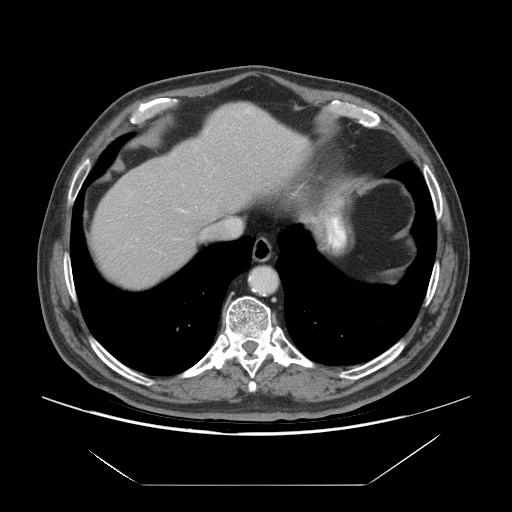
Contrast-enhanced abdominal CT (liver protocol), one axial slice. Position 61 of 75 along the scan axis. Reconstruction kernel STANDARD. 140 kVp. Soft-tissue window (W 400 / L 40 HU). 2.5 mm slice thickness. 512 × 512 image matrix, field of view 420 × 420 mm. Case-level facts recorded for this patient, not image findings: diagnosis: hepatocellular carcinoma (patient treated with transarterial chemoembolisation; whether this scan precedes or follows treatment is not stated here); TNM stage (as recorded): Stage-I; Child-Pugh class: A; tumour differentiation: well differentiated; tumour nodularity: uninodular.
Structures marked on this image (semi-automatically segmented with operator editing):
- liver parenchyma outside the tumour (the mass and vessels are separate outlines, so this box may not span the whole liver): bounding box (x1, y1, x2, y2) in pixels: (92, 104, 308, 288)
- liver vessels: (181, 110, 249, 212)